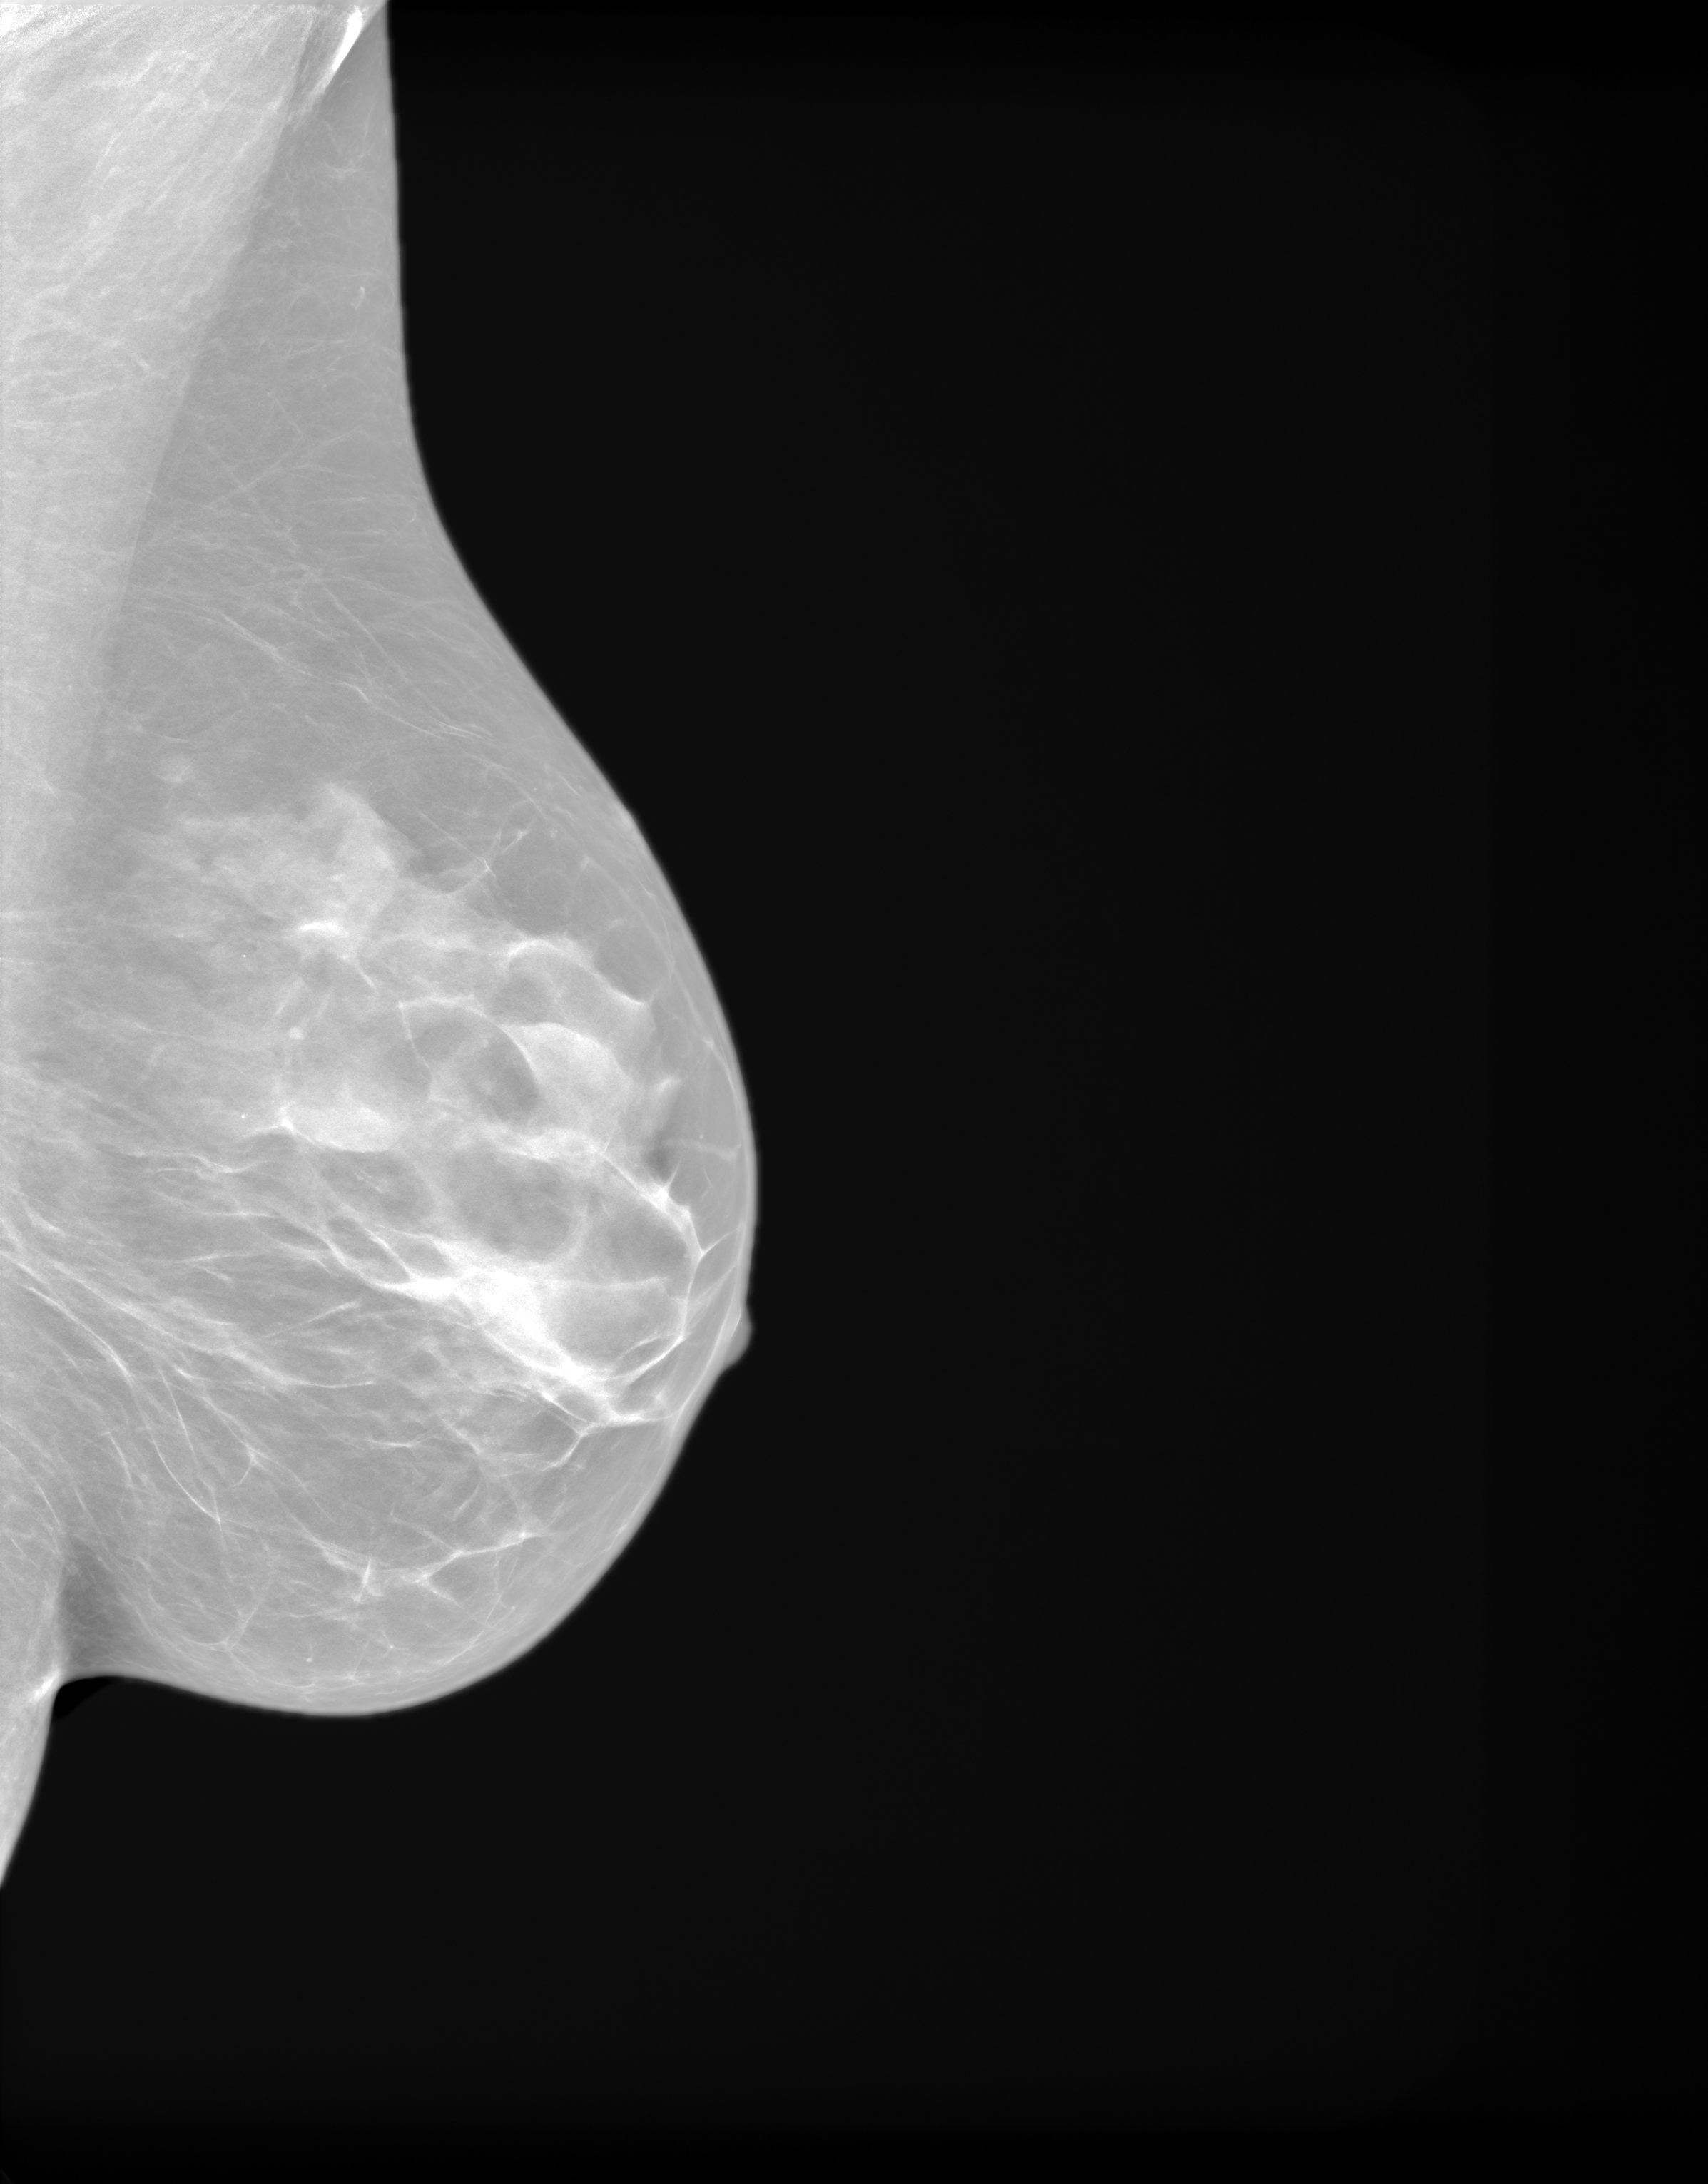
Annual screening mammography examination. Female patient, age 52 years.
Image type: synthesized 2-D view from tomosynthesis. Breast: left. Projection: mediolateral oblique (MLO) view.